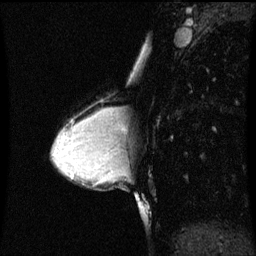
Breast MRI (dynamic contrast-enhanced), one sagittal slice. Dynamic contrast-enhanced series, image 2 of 3 at this slice position (ordered by acquisition). 1.5 T. TE 4.2 ms, TR 8.9 ms. 256 × 256 image matrix, field of view 200 × 200 mm. Patient: female, 33 years. From the clinical record (not read from this slice): setting: breast cancer imaged before/during neoadjuvant chemotherapy; receptor status: HER2-positive.
Structures marked on this image (semi-automatically segmented with operator editing):
- analysis volume of interest (the breast-tissue region the enhancement analysis was run in; not a lesion): bounding box [x1, y1, x2, y2] px = [107, 108, 119, 147]
- tumour enhancement mask (voxels above the 70 % enhancement threshold inside the analysis volume of interest): [107, 108, 119, 131]